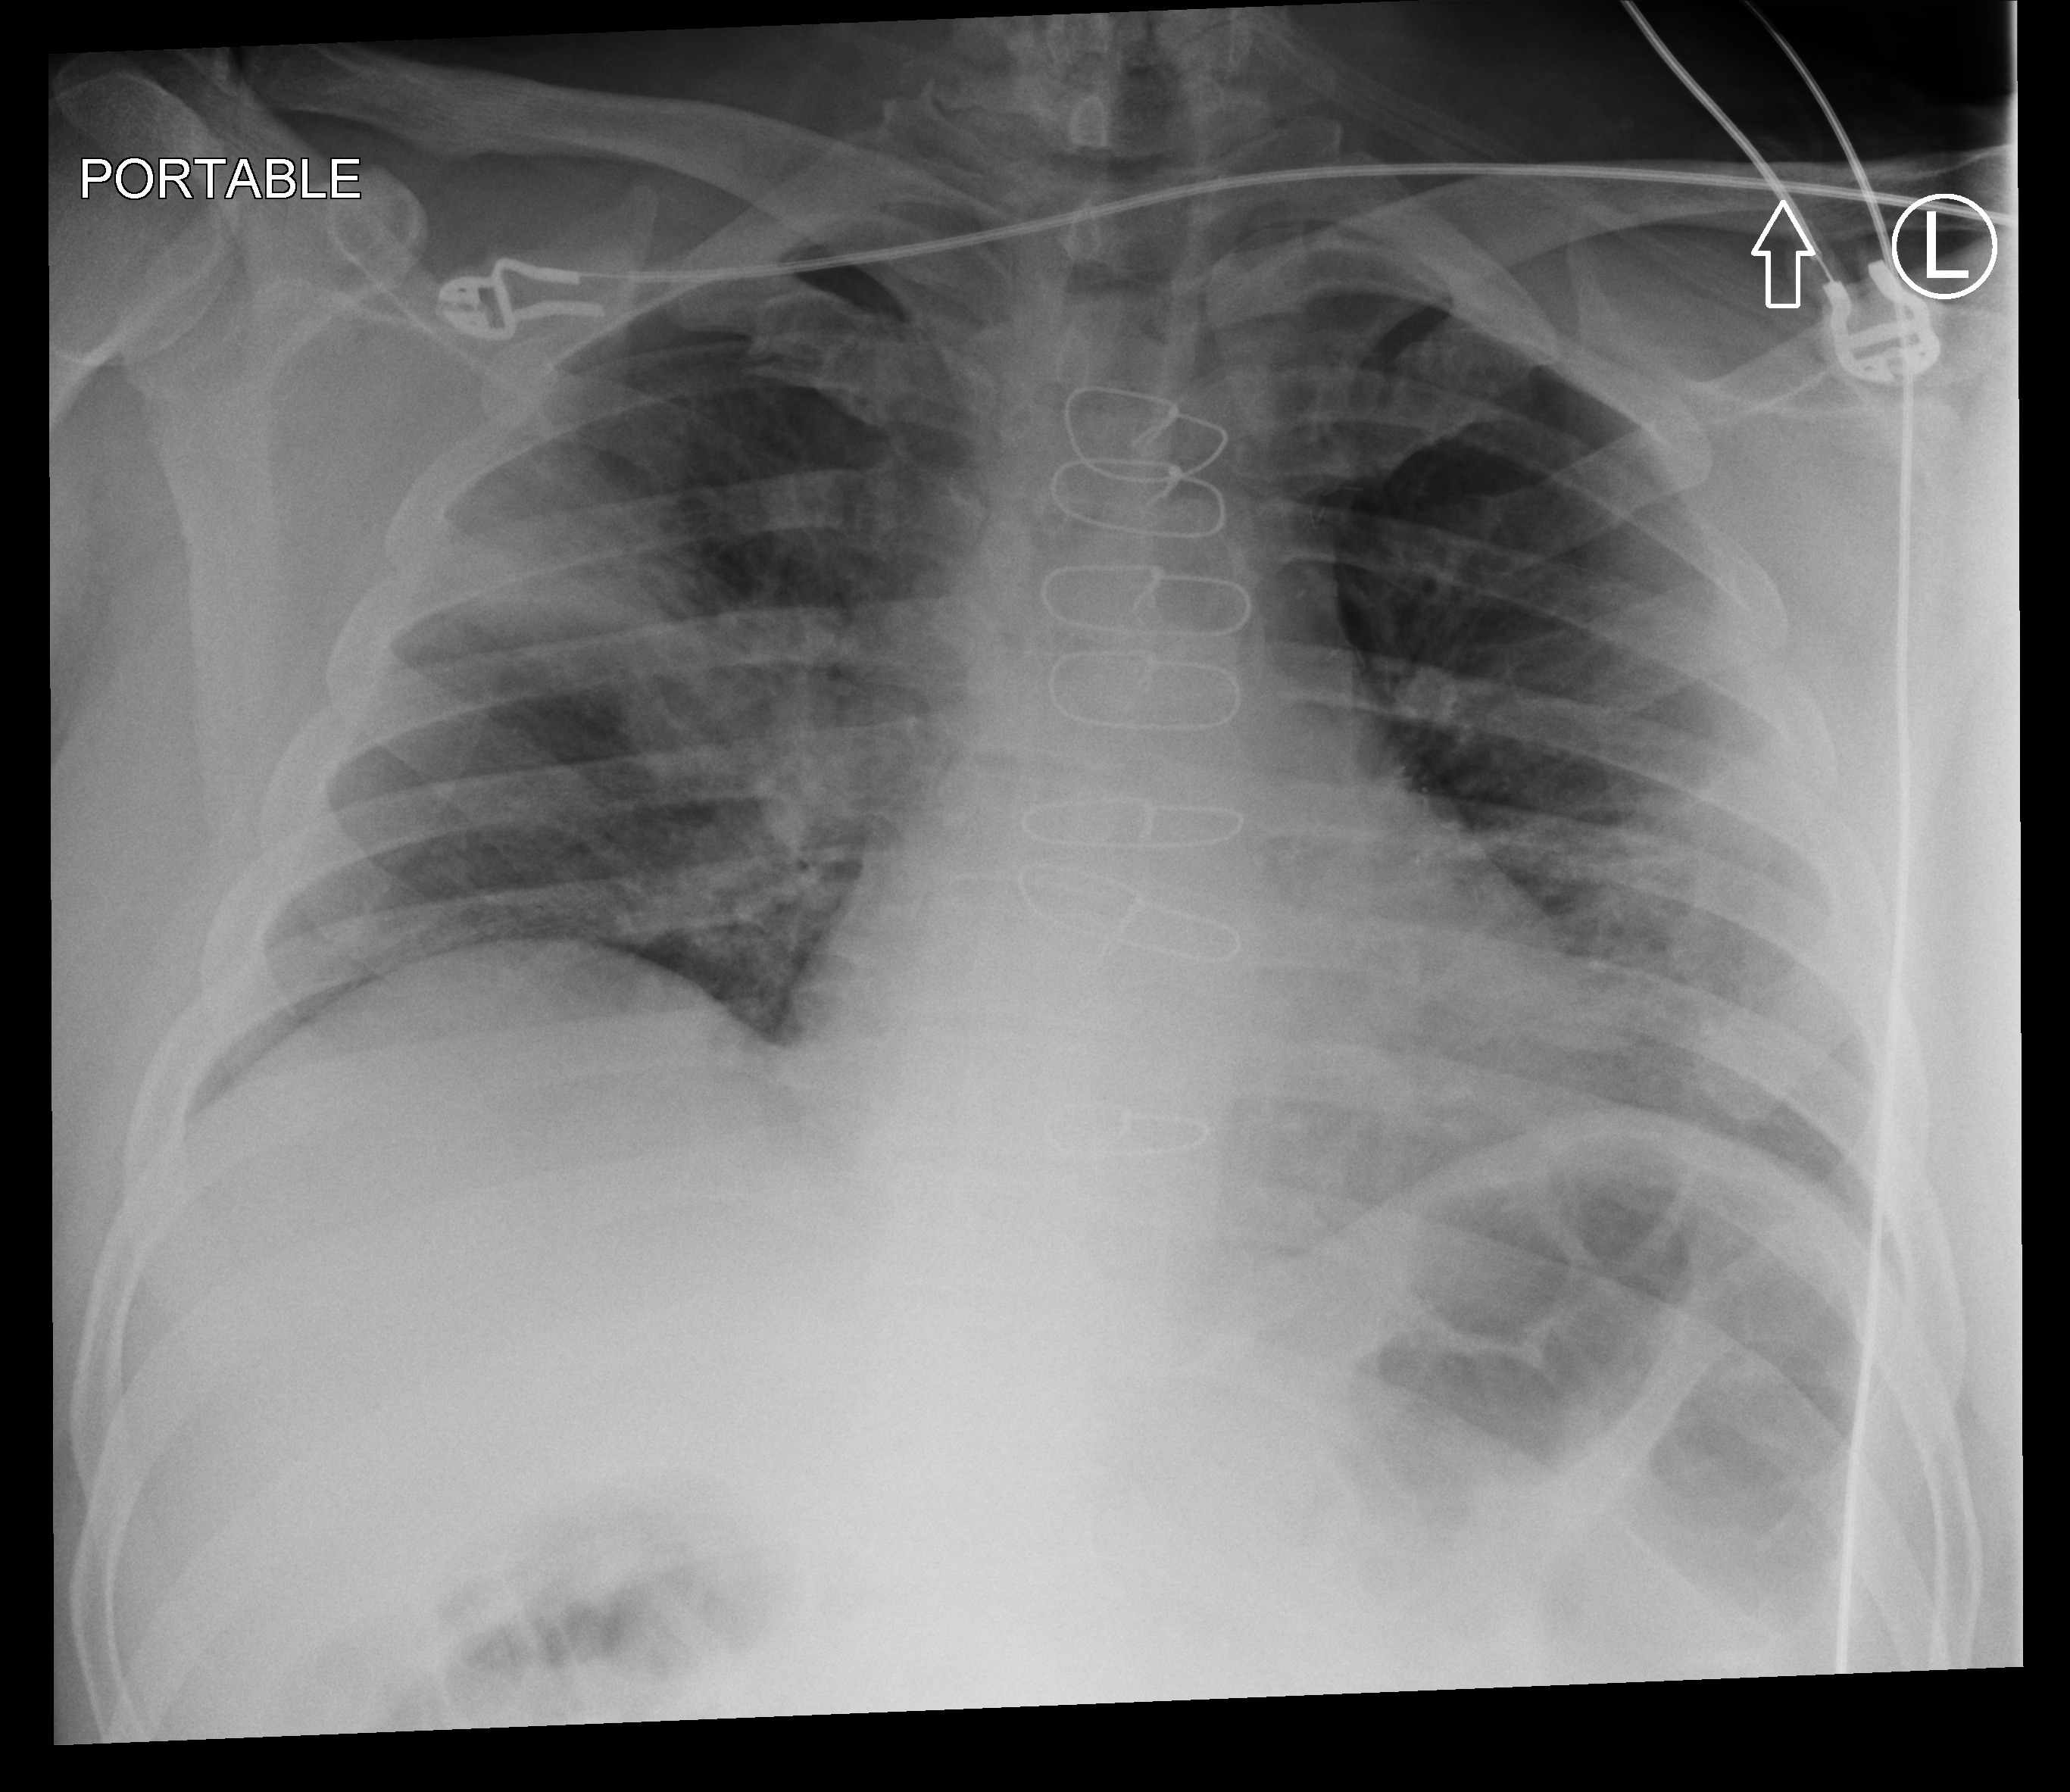
Portable chest radiograph; anteroposterior (AP) projection. Patient hospitalised with COVID-19; male, aged 60–74 years.
From the hospital-stay record, not from the radiograph (when in the stay this image was taken is not recorded): mechanically ventilated during this hospital stay: yes; chronic kidney disease (admission record): no.